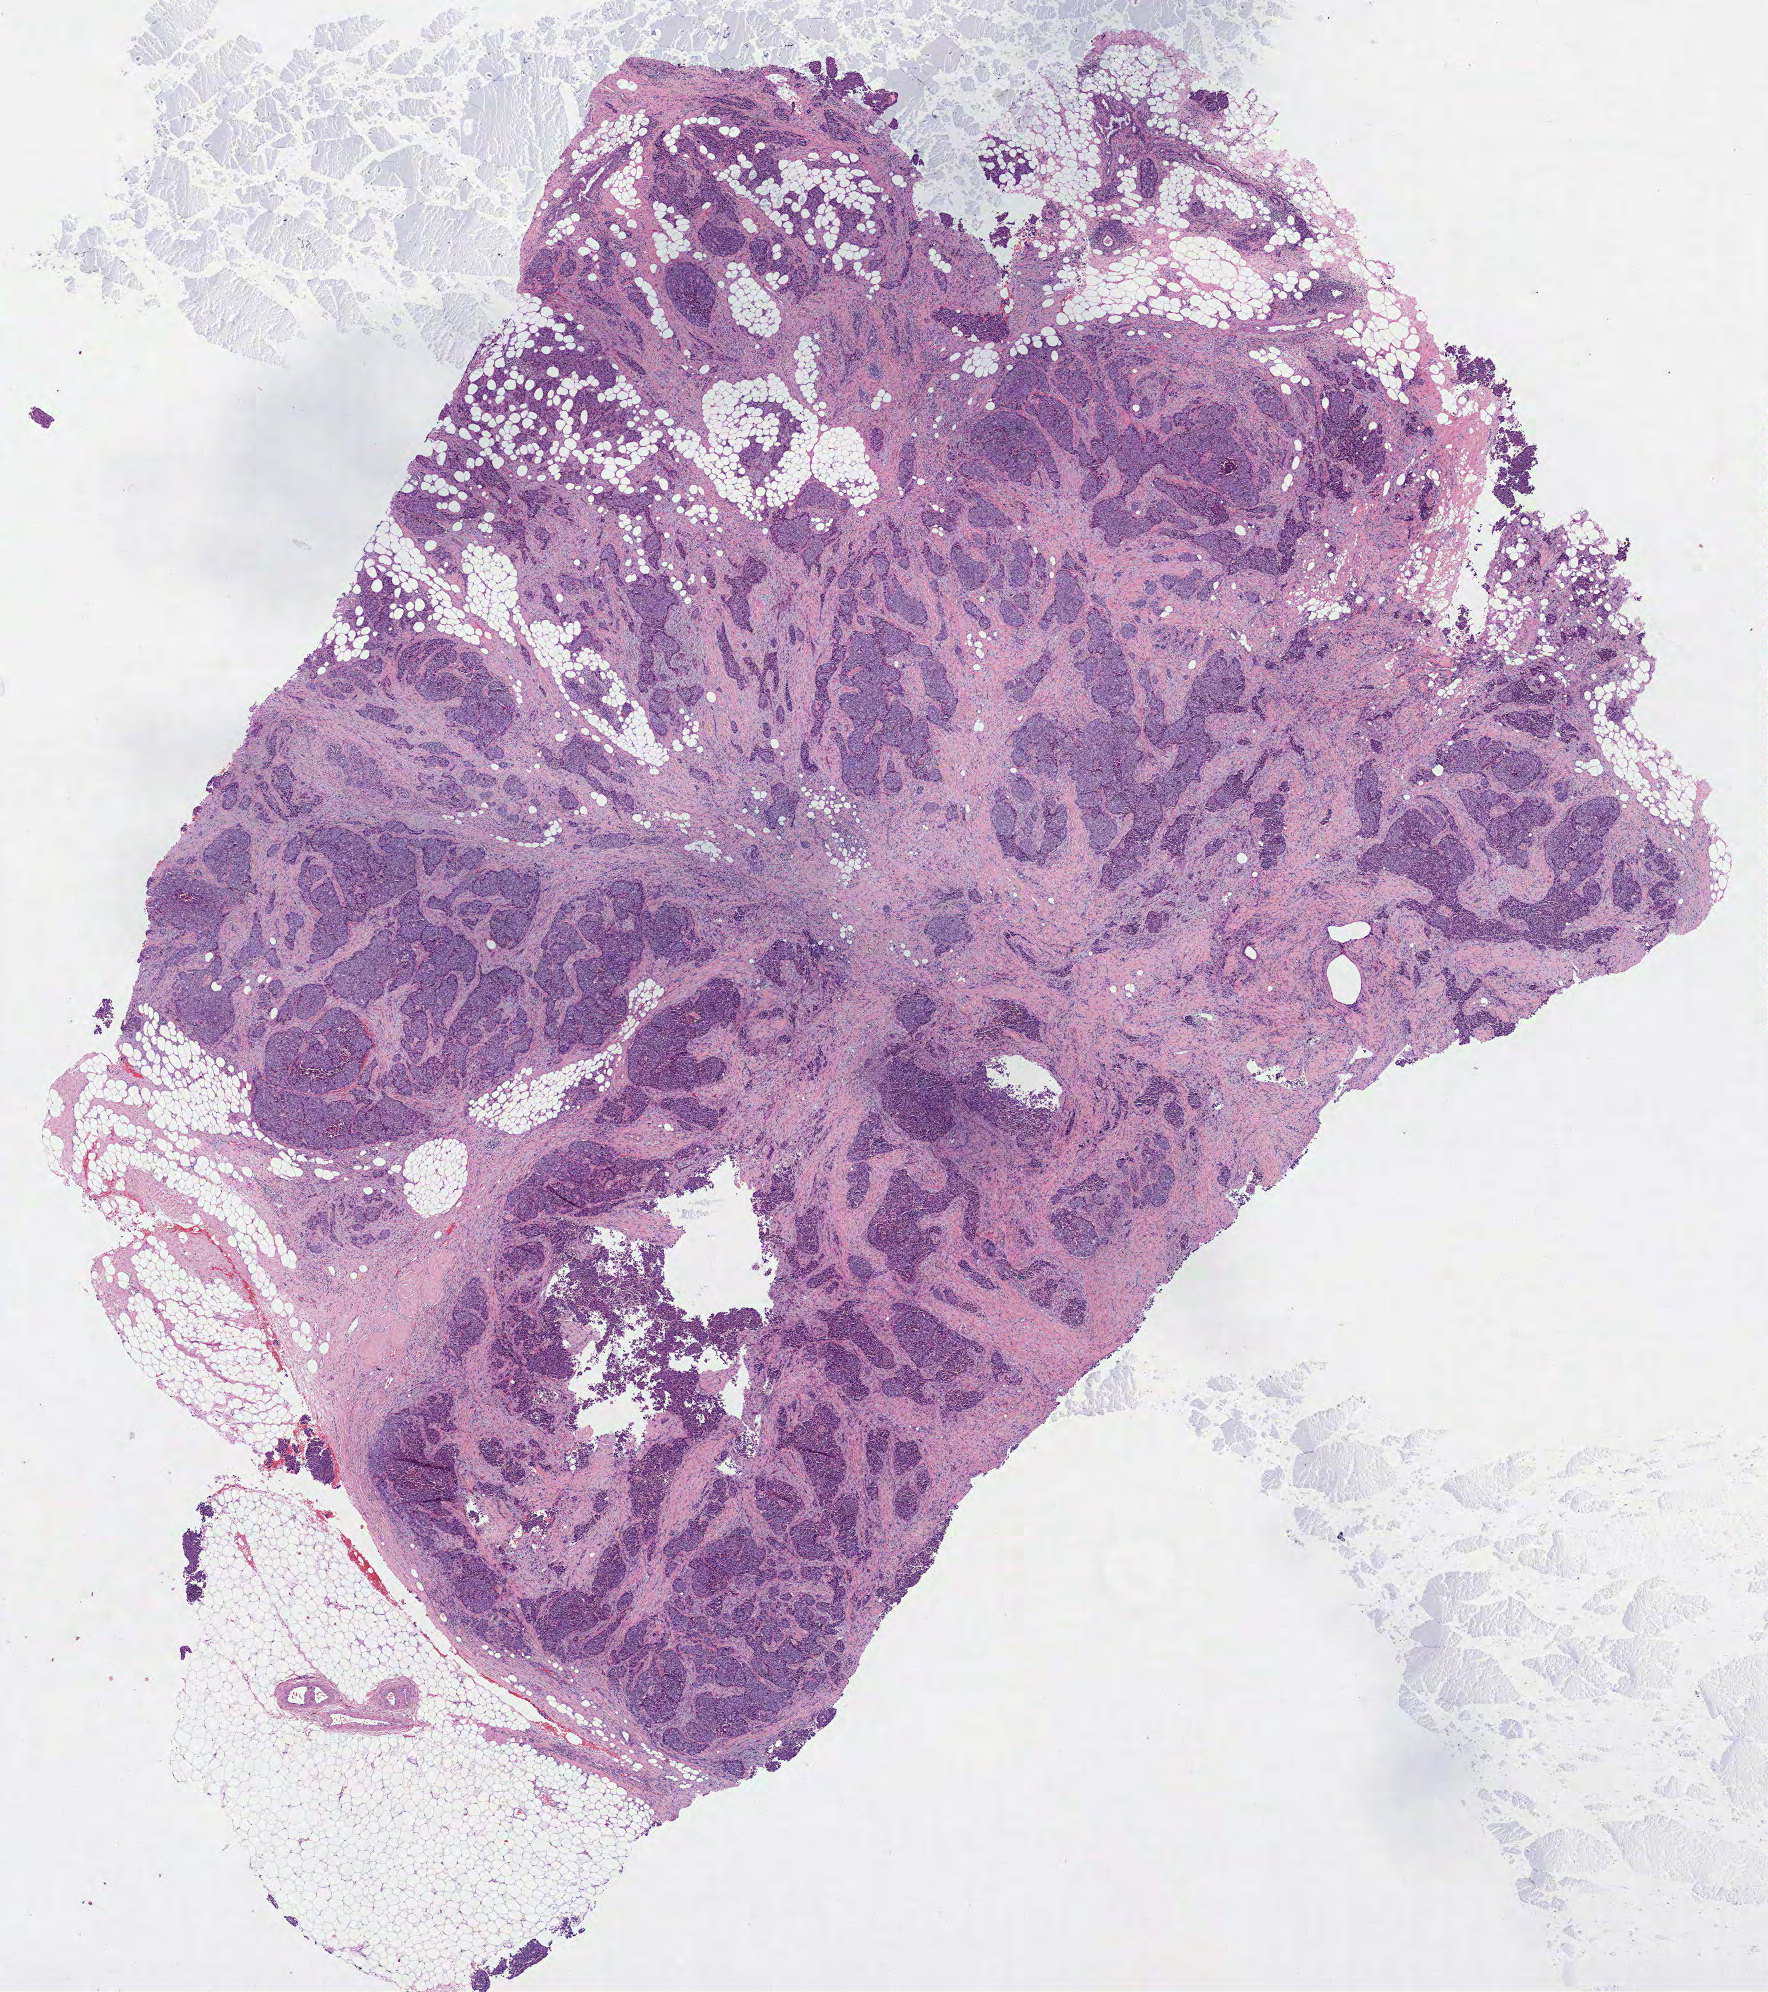
Hematoxylin and eosin (H&E) stained whole-slide image, a low-resolution overview of the entire scanned area, about 14.3 x 16.1 mm (slide scanned at 40x); formalin-fixed paraffin-embedded (FFPE) diagnostic section; breast, primary tumour sample. Female, age 74 years at initial diagnosis.
- histologic diagnosis: Infiltrating duct carcinoma, NOS
- AJCC pathologic stage: IIB
- laterality: left